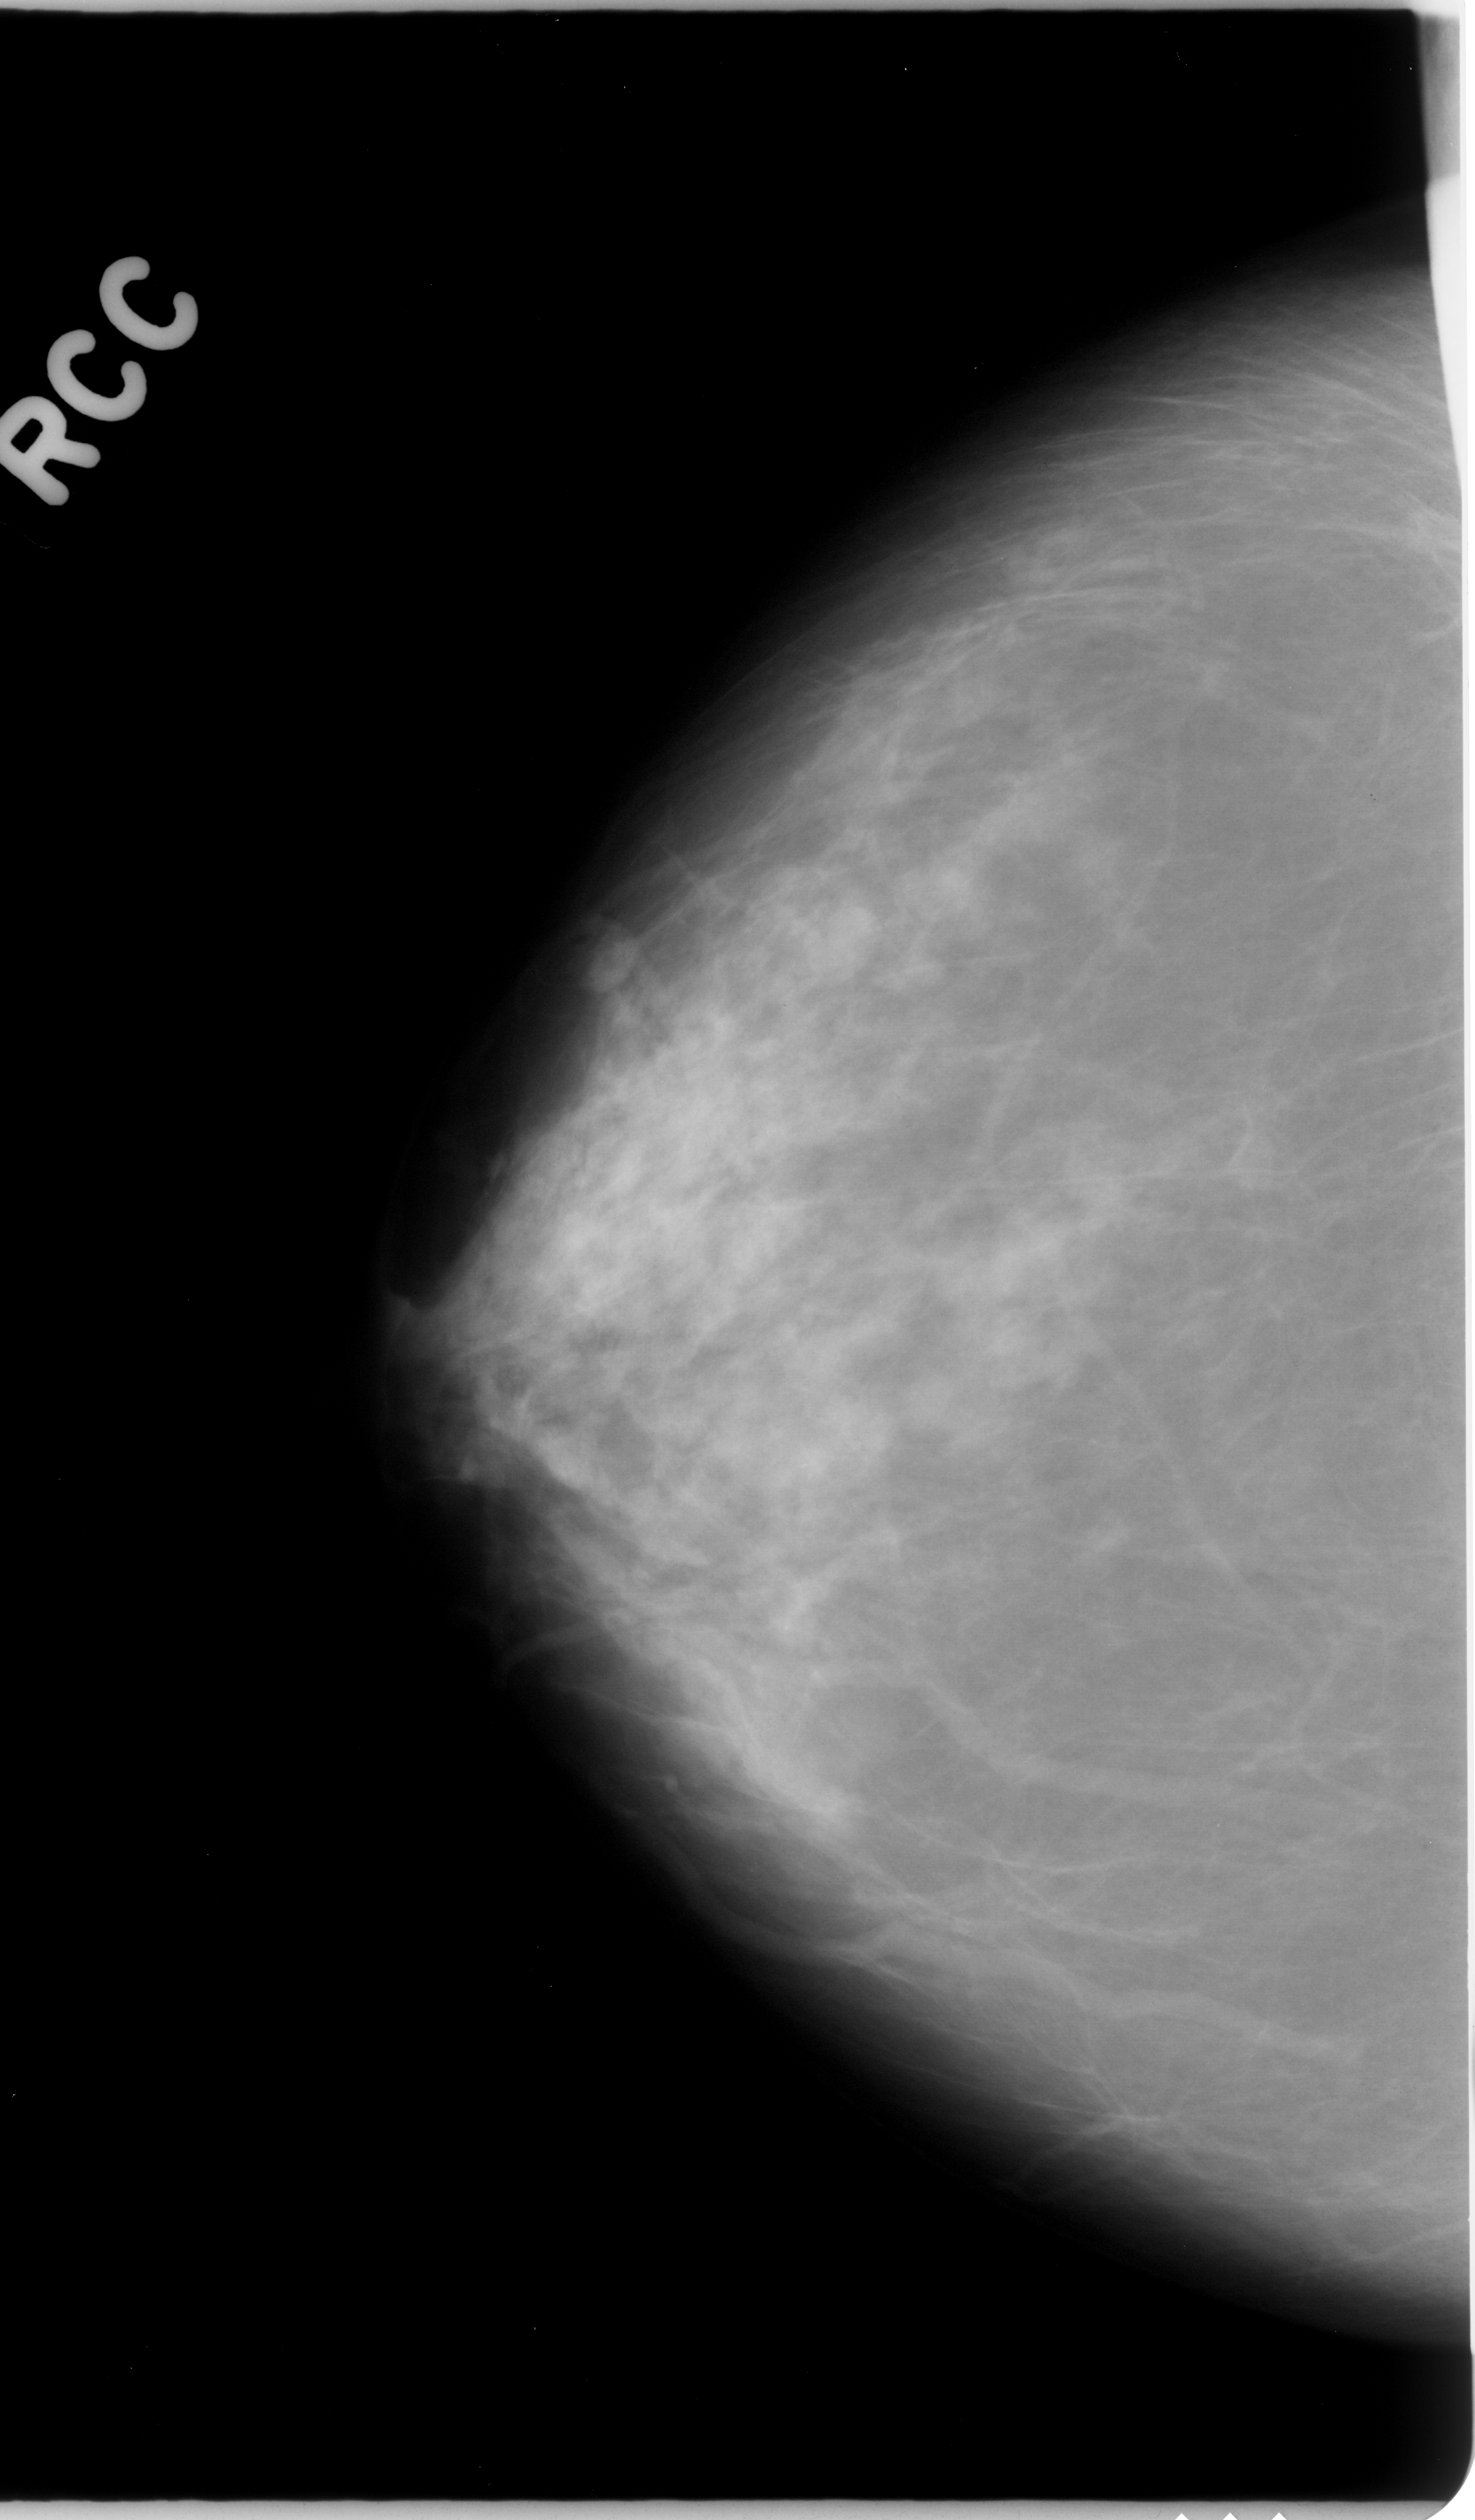
Digitized screen-film mammogram; right breast; CC view; 1475 × 2520 image matrix.
Expert-marked regions of interest on this film, with their recorded descriptors:
- mass, shape lobulated, margins circumscribed; BI-RADS assessment category 3; subtlety rating 5 on a 1 (subtle) to 5 (obvious) scale; pathology (as recorded): benign: box from (x=765, y=878) to (x=896, y=1003) px